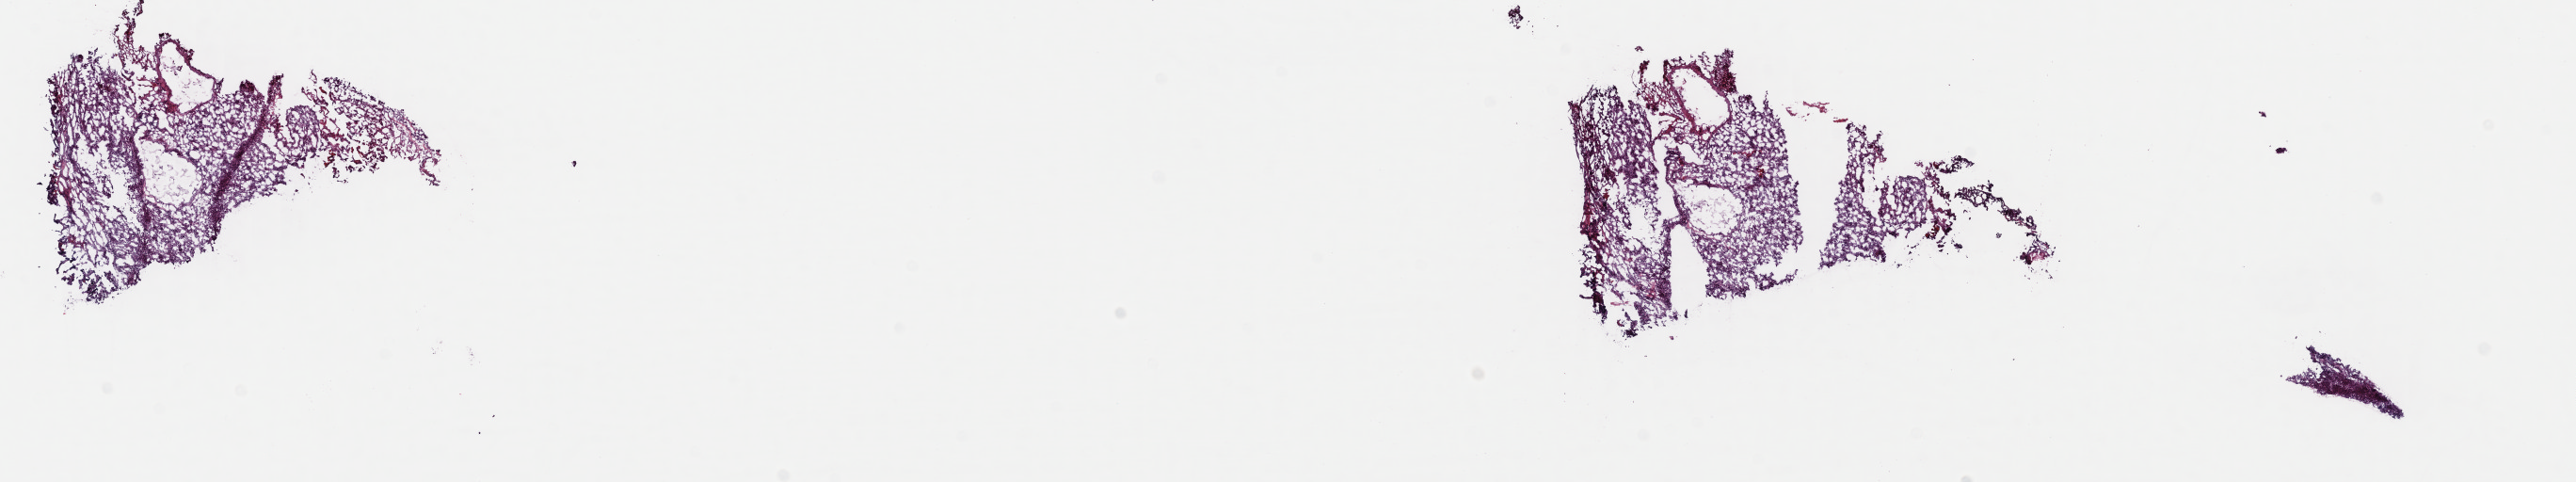
H&E-stained whole-slide image — a low-resolution overview of the entire scanned area, about 21.5 x 4.0 mm, frozen section, metastatic tumour sample, sampled site: brain. Patient: male, age at initial diagnosis 77 years. Composition of this section per pathologist review: tumour cells 100%, tumour nuclei 90%, normal cells 0%, stromal cells 0%, necrosis 0%. Infiltration values recorded for this section: lymphocyte infiltration 0%, monocyte infiltration 0%, neutrophil infiltration 0%.
* this section: metastatic tumour tissue
* patient diagnosis: Malignant melanoma, NOS